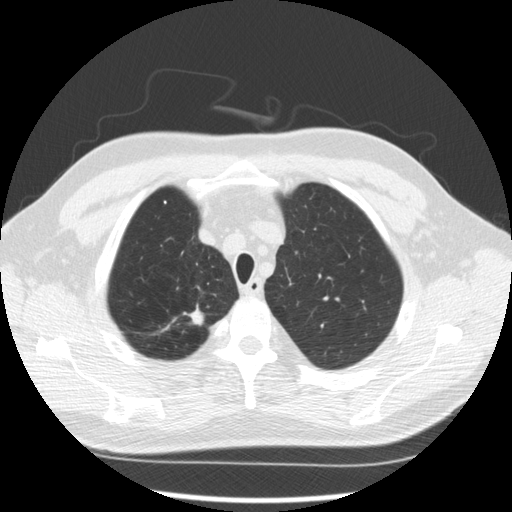
Low-dose screening chest CT, axial slice, second screening round (one year after baseline), lung window (W 1500 / L -600 HU), 120 kVp. Male participant, aged 64 years at enrolment. Former smoker at enrolment.
Expert reader's lesion annotation, box from (x=173, y=300) to (x=216, y=336) px. The screening reader recorded 3 non-calcified nodules or masses ≥4 mm on this exam (right upper lobe, right upper lobe, right upper lobe); which of them this box marks is not recorded. Lung cancer was diagnosed 411 days after this screen: adenocarcinoma, NOS, right upper lobe, moderately differentiated (G2), stage IA (AJCC 6th edition), 14 mm at pathology.